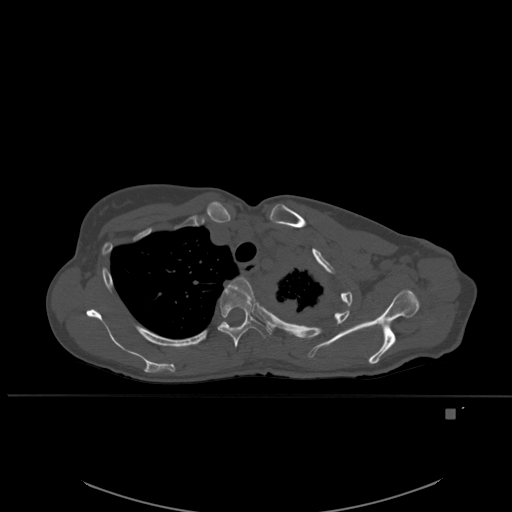
CT including the spine, one axial slice; position 414 of 537 along the scan axis; bone window (W 1800 / L 400 HU); 1.5 mm slice thickness; 512 × 512 image matrix. Female patient, age 45 years. From the clinical record (not read from this slice): primary cancer: lung.
Outlined on this slice (semi-automatic segmentation, software-assisted and operator-edited):
- T3 vertebra: bounding box <228,277,254,304> (left, top, right, bottom; pixels)
- T4 vertebra: <217,288,270,348>